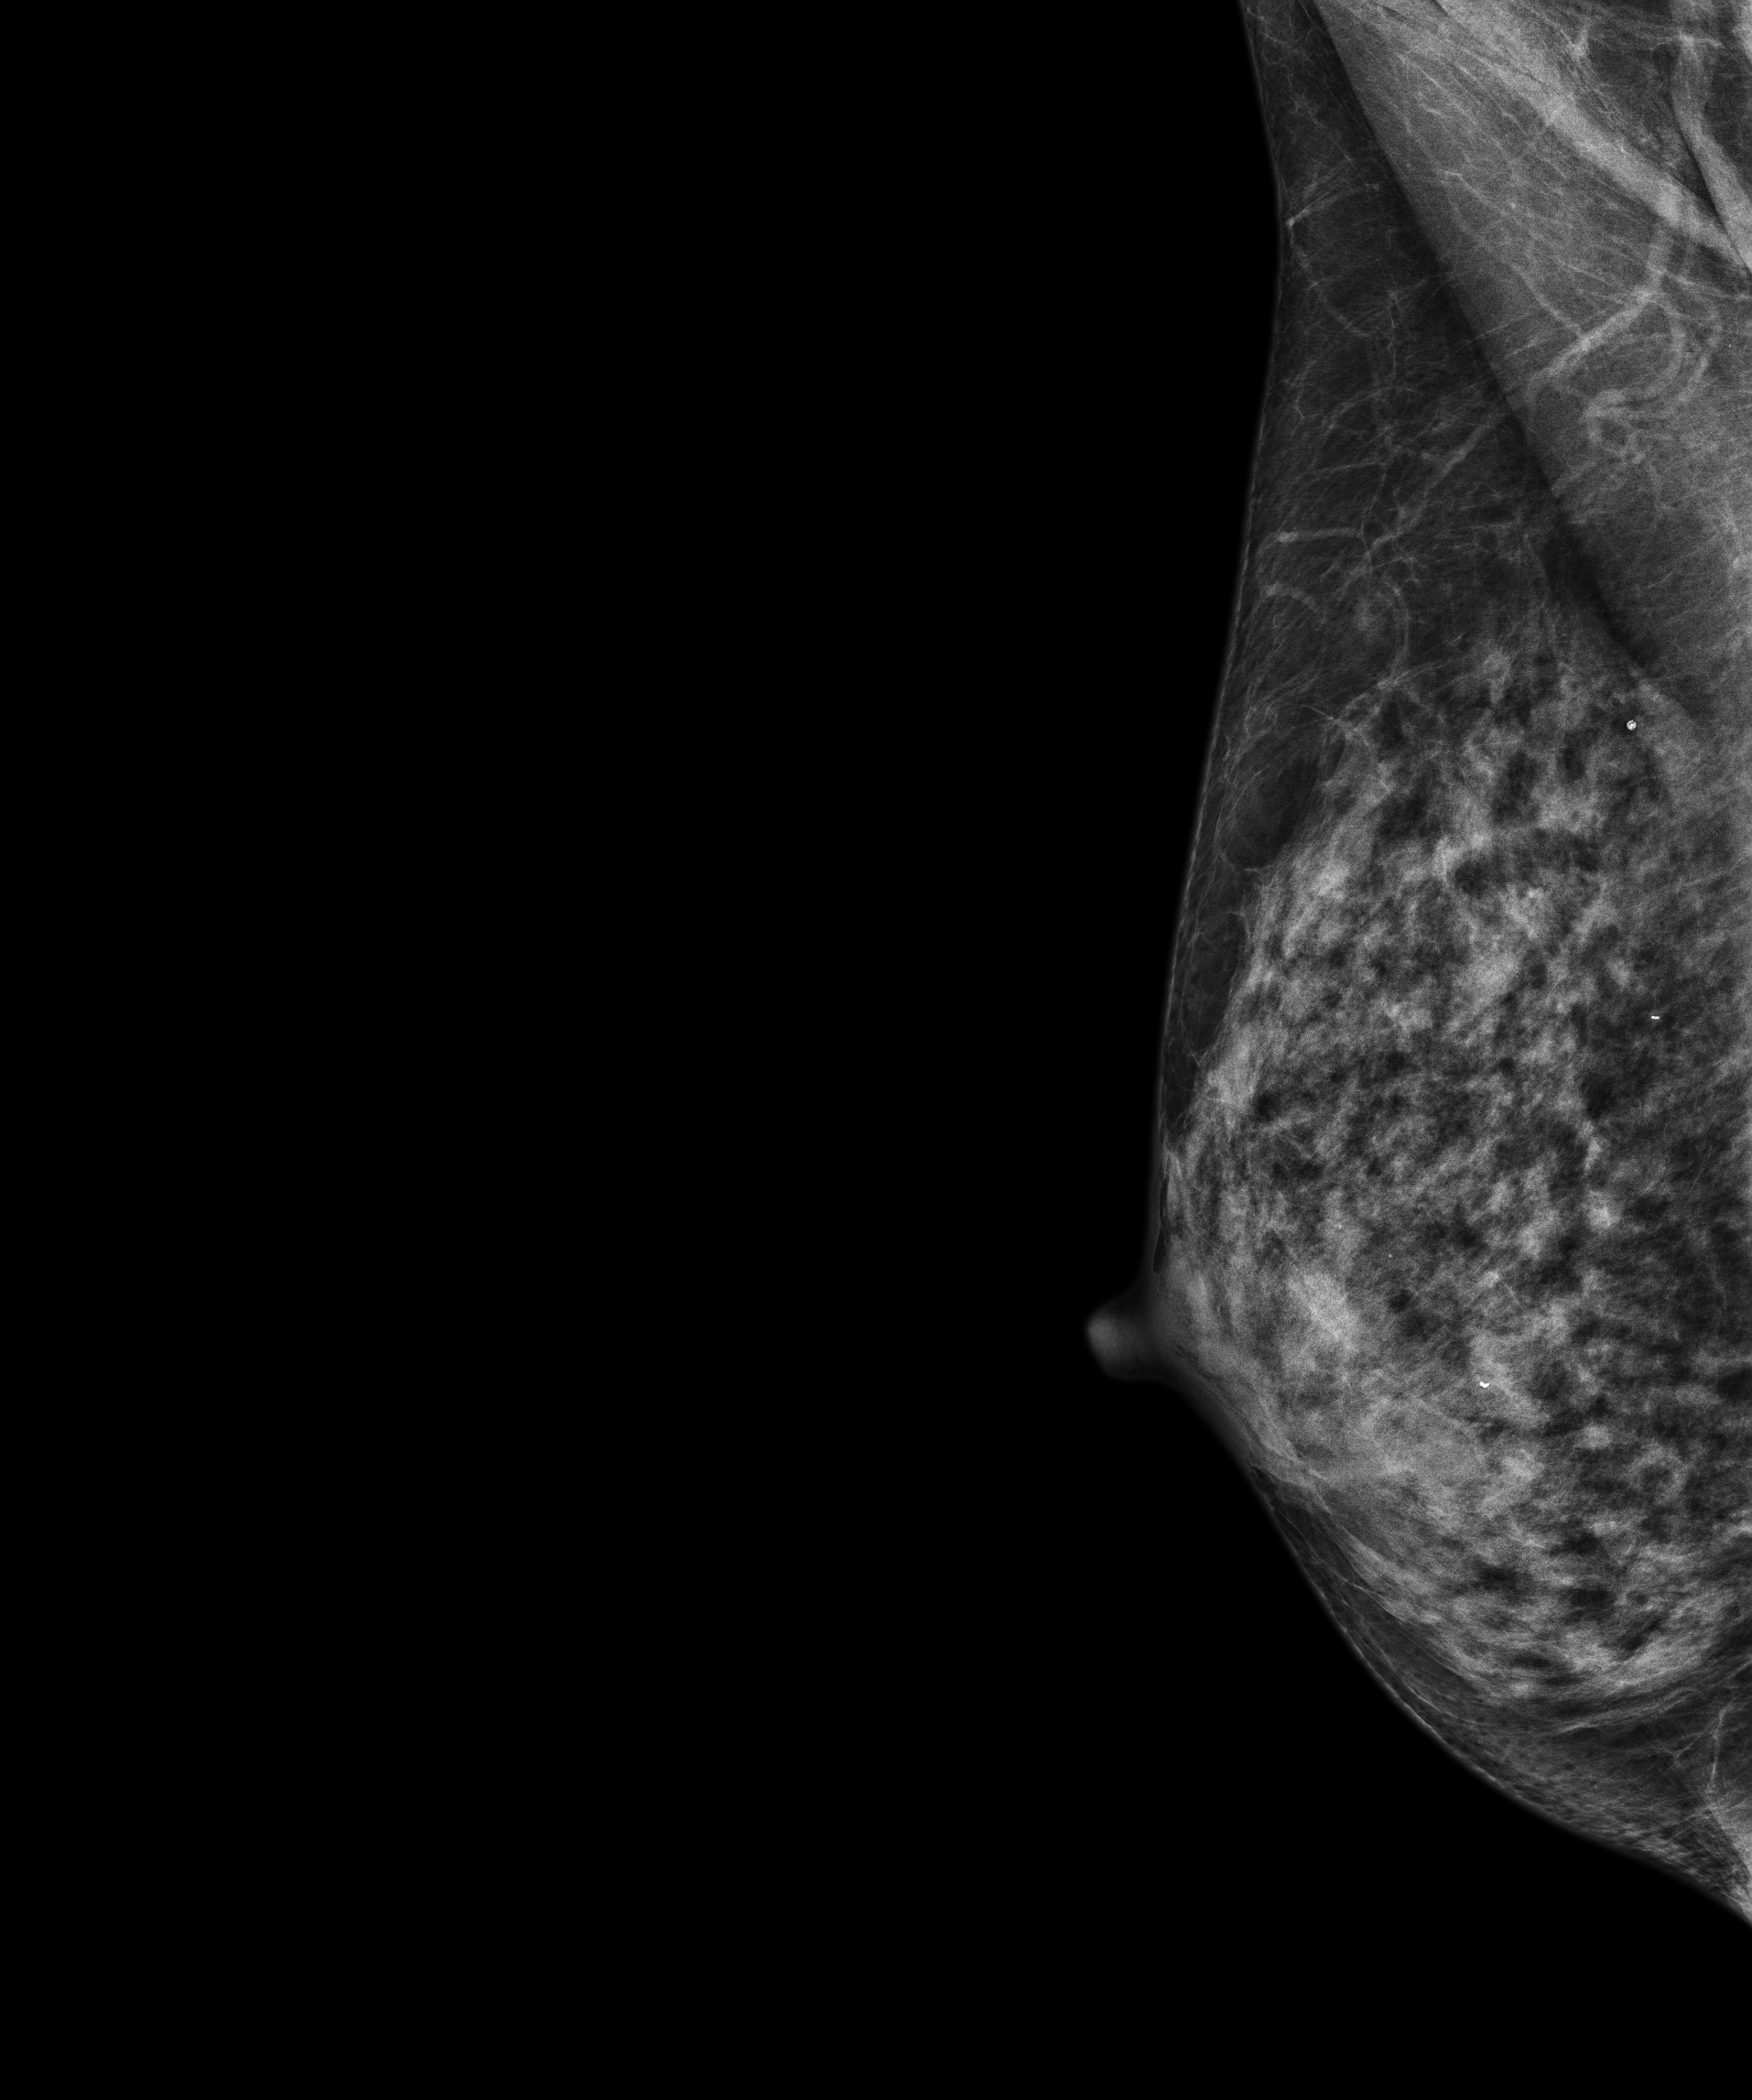
Screening examination, compressed breast thickness 37.2 mm, system: Senographe Pristina. Patient aged 68 years (female).
Image type: full-field digital mammogram. Breast: right. Projection: medio-lateral oblique projection.